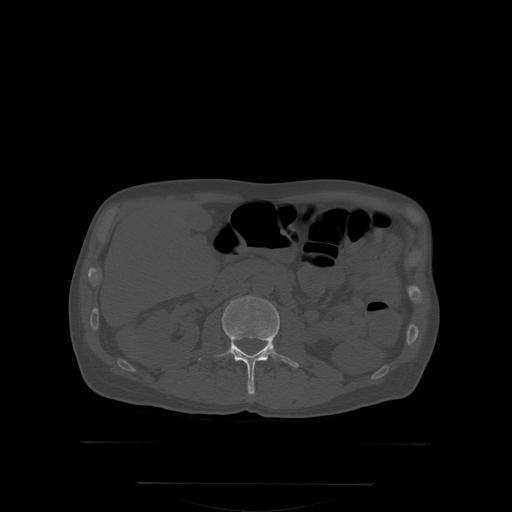
CT including the spine, one axial slice. Slice 137 of 350 in the series (ordered by position). Bone window (W 1800 / L 400 HU). 2.5 mm slice thickness. 512 × 512 image matrix. Male patient, age 58 years. From the clinical record (not read from this slice): primary cancer: prostate; vertebrae with lytic lesions (as recorded): L1.
Structures marked on this image (semi-automatically segmented with operator editing):
- L2 vertebra: bounding box (x1, y1, x2, y2) in pixels: (198, 296, 299, 396)